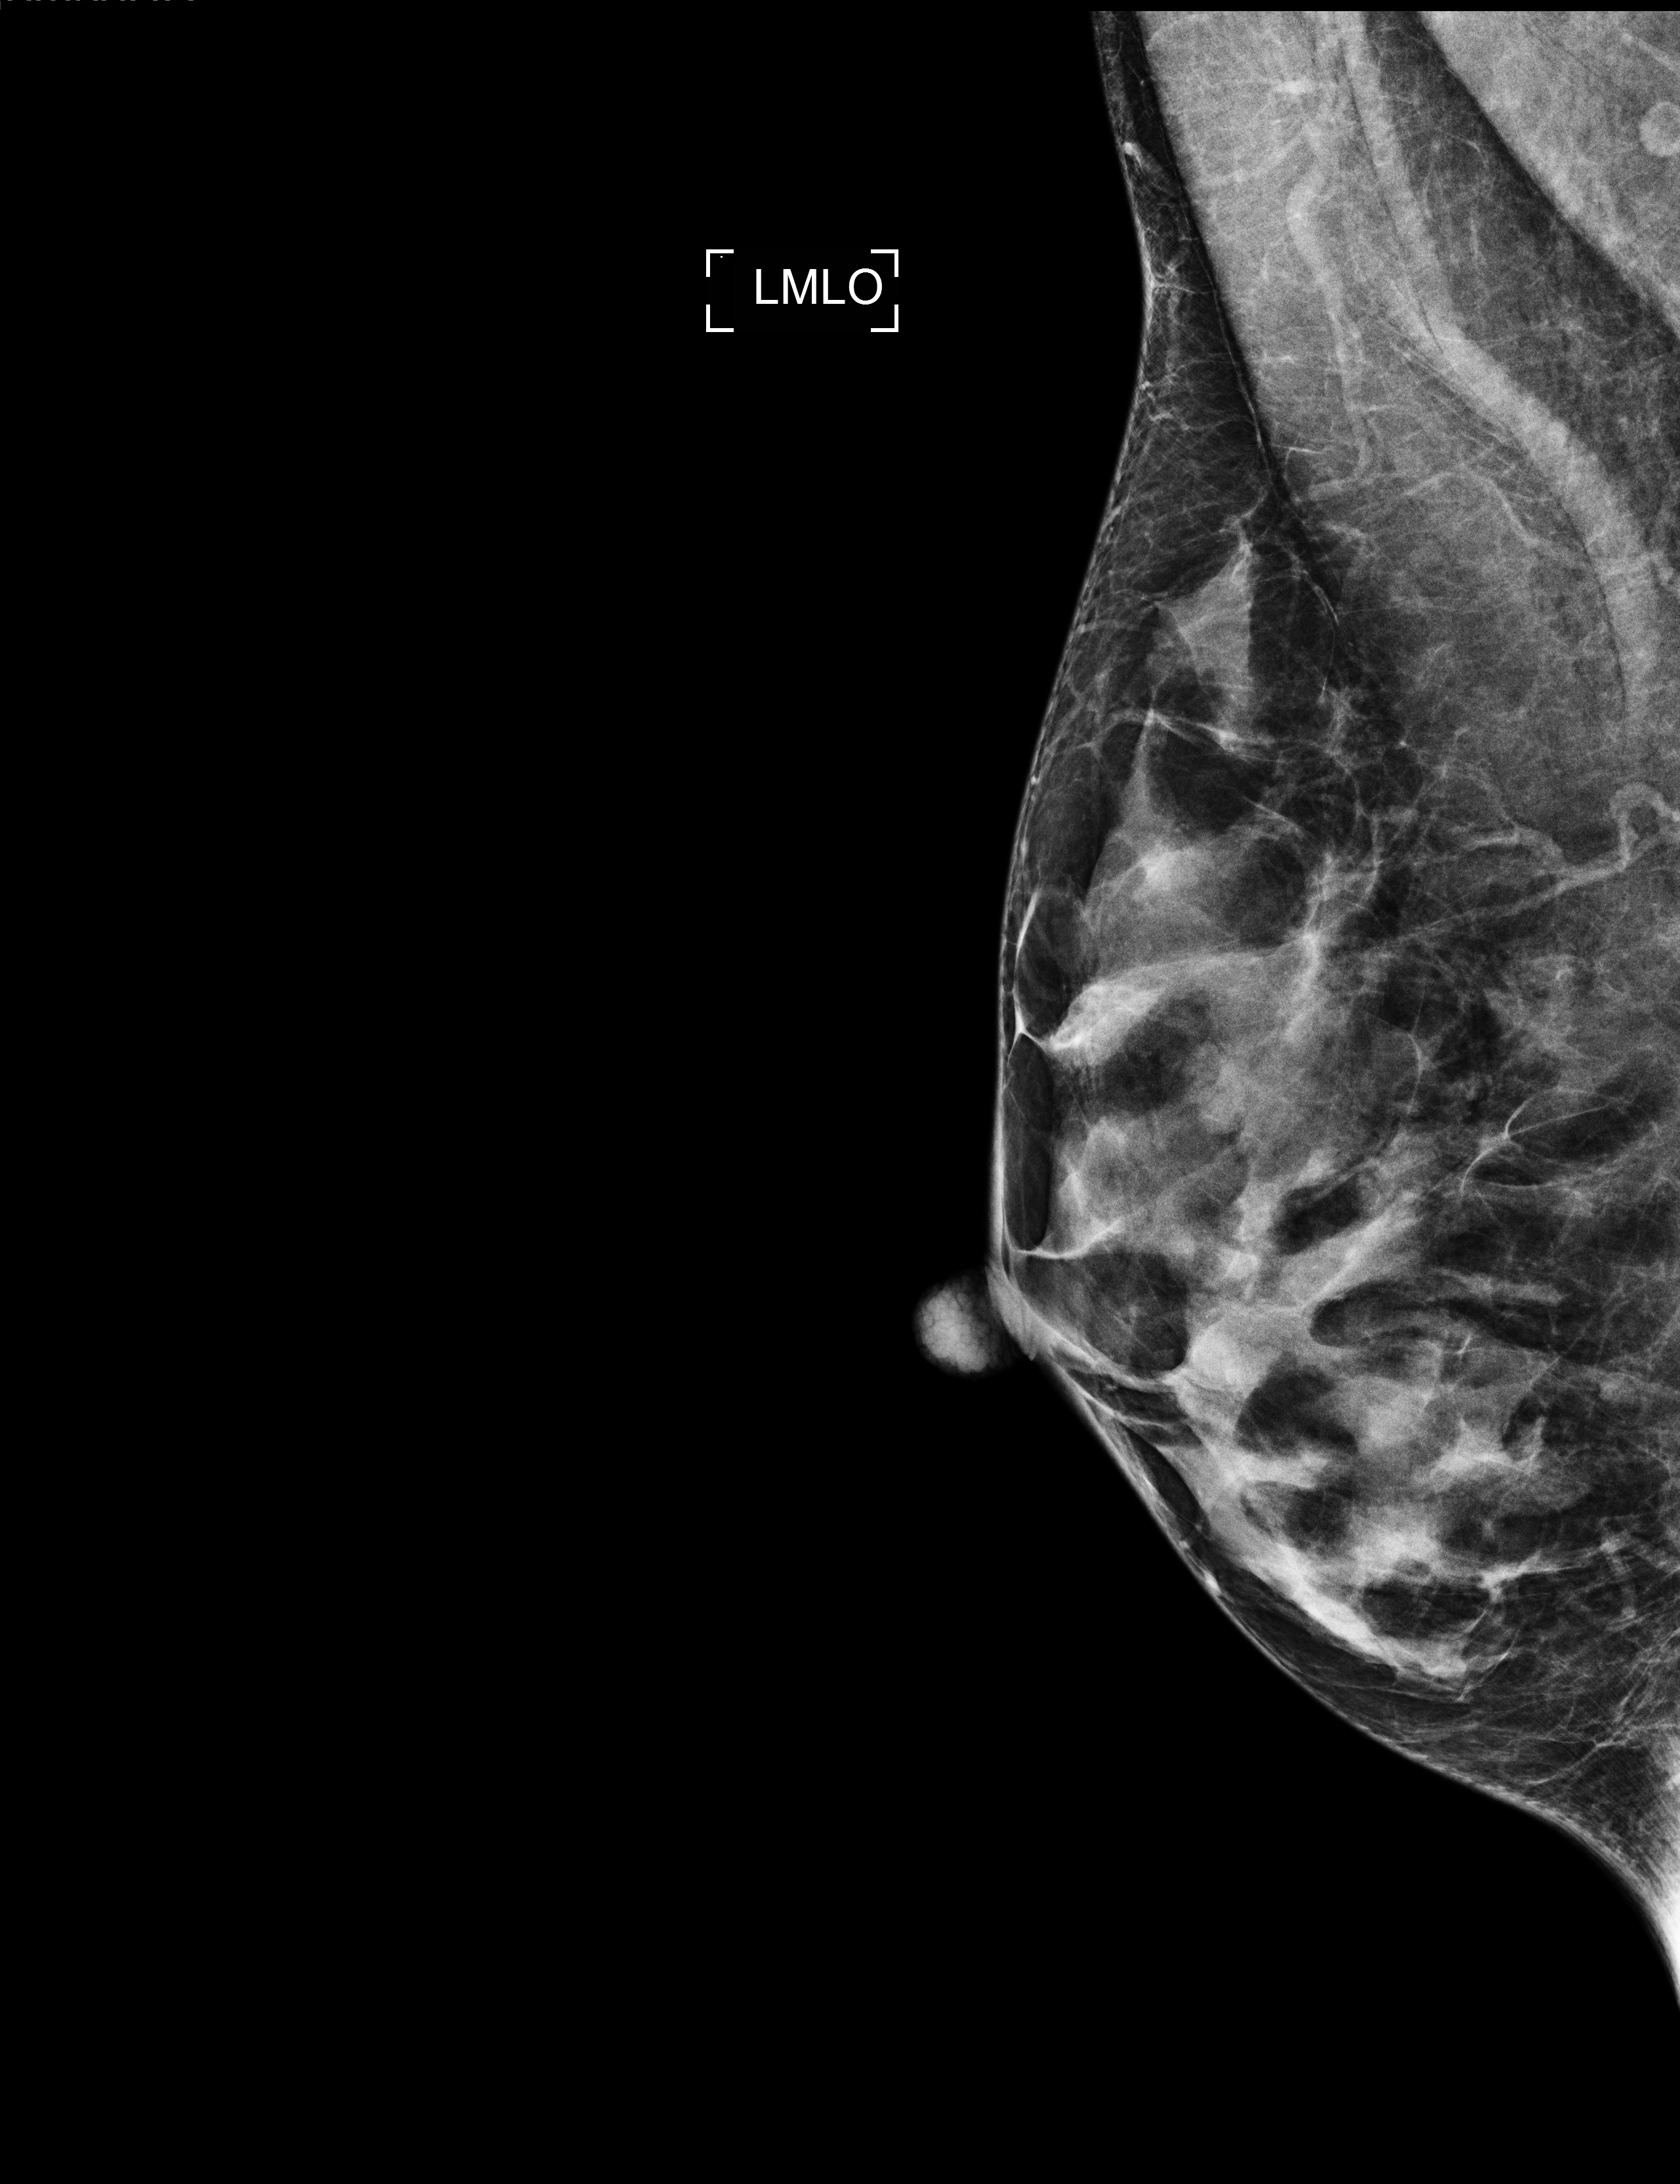
Screening examination, compressed breast thickness 22 mm, system: Selenia Dimensions. Patient aged 54 years (female).
Image type: full-field digital mammogram. Breast: left. Projection: mediolateral oblique (MLO) view.